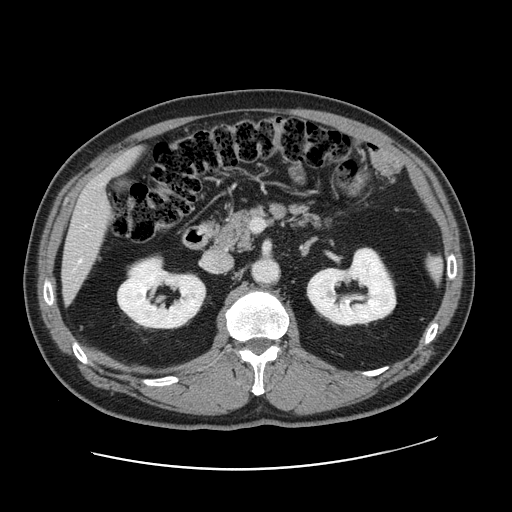
Contrast-enhanced abdominal CT, one axial slice; slice 79 of 178 in the series (ordered by position); intravenous contrast given; soft-tissue window (W 400 / L 40 HU); 512 × 512 image matrix, field of view 403 × 403 mm. Male patient, age 63 years. From the clinical record (not read from this slice): diagnosis: colorectal cancer liver metastases, imaged before liver resection; multiple liver metastases: yes; largest metastasis: 8 cm; disease in both lobes: yes.
Annotated regions visible in this slice (expert manual segmentation):
- hepatic veins: bounding box [x1, y1, x2, y2] px = [79, 259, 82, 261]
- liver: [63, 153, 137, 297]
- planned liver remnant (the part of the liver to remain after resection): [111, 153, 137, 170]